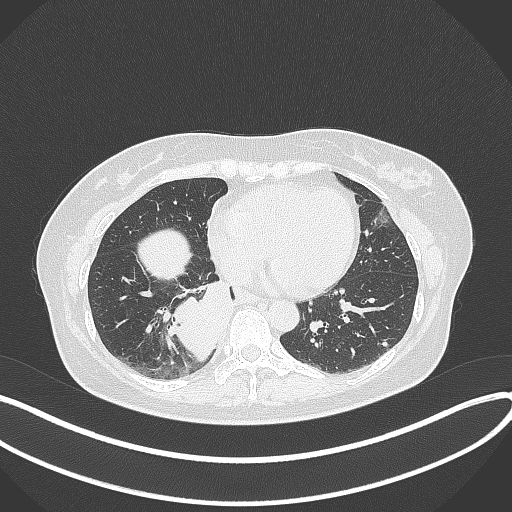
Chest CT, one axial slice; position 124 of 331 along the scan axis; 120 kVp; lung window (W 1500 / L -600 HU); 512 × 512 image matrix, field of view 400 × 400 mm. Female patient, age 54 years. Case-level facts recorded for this patient, not image findings: clinical TNM (as recorded): T4 N0 M0.
Outlined on this slice (bounding box drawn by a radiologist):
- lung tumour (recorded histology: adenocarcinoma): bounding box (x1, y1, x2, y2) in pixels: (165, 279, 233, 367)